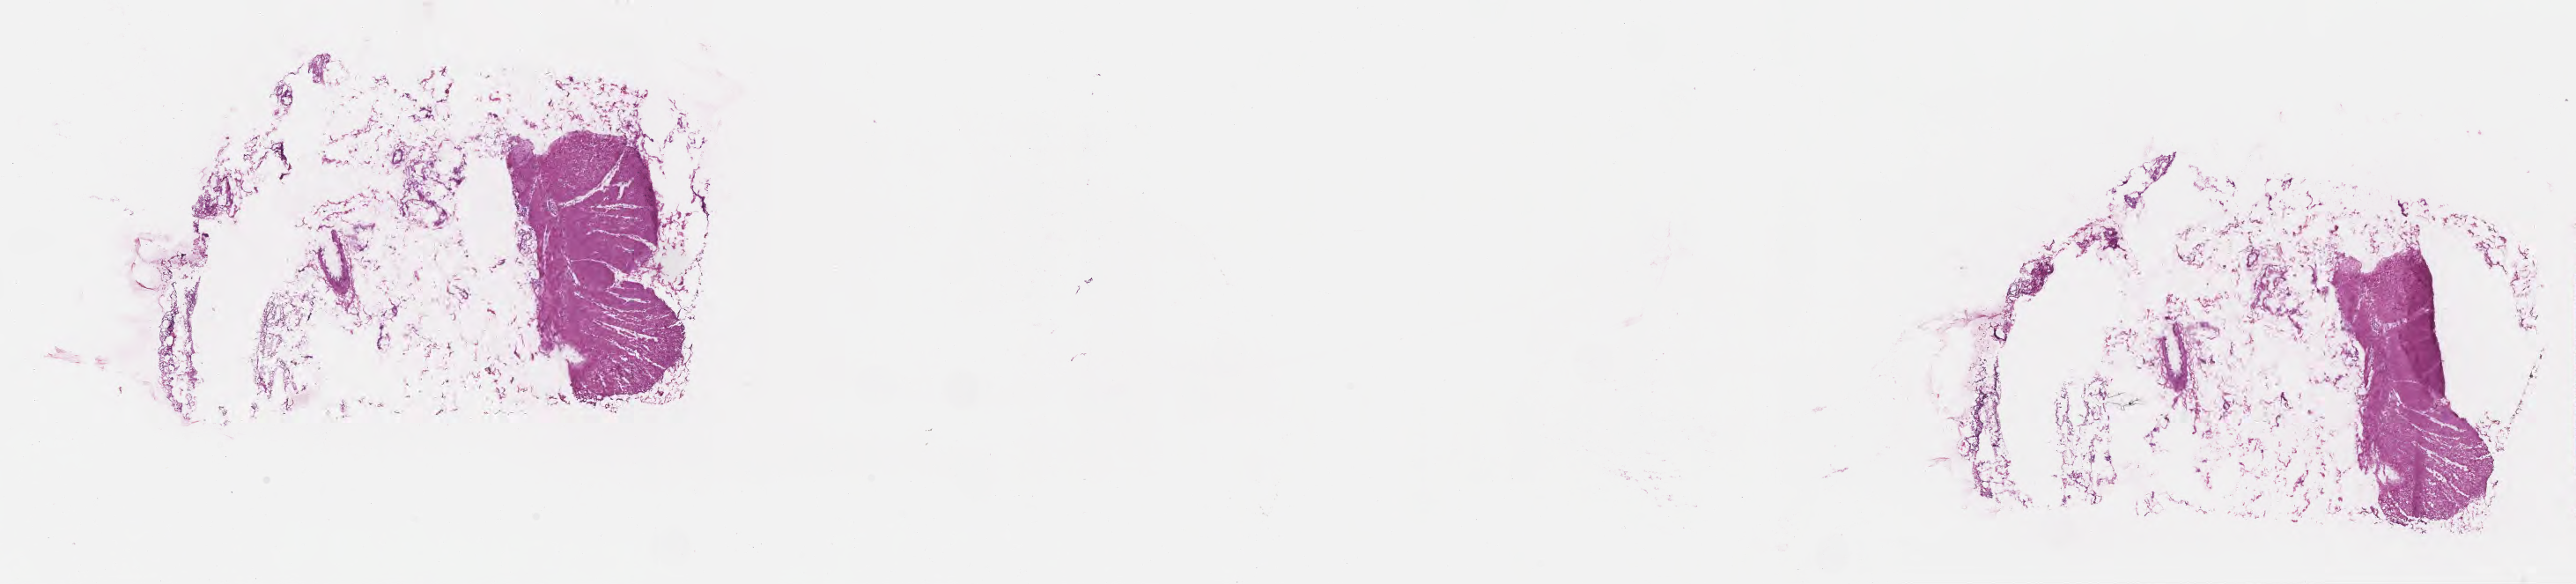
Digitized H&E-stained section — whole scanned area (about 23.6 x 5.4 mm) shown as a low-resolution overview; frozen section (tissue freezing medium); specimen: normal-tissue sample (non-tumor) from a patient with adenocarcinoma, NOS; anatomic site: sigmoid colon. Male, age 82 years at initial diagnosis. Pathologist review of this section (percent, as recorded): tumor cells 0%, tumor nuclei 0%, stromal cells 0%, necrosis 0%, normal cells 100%. Inflammatory infiltration, as recorded: lymphocyte infiltration 0%, monocyte infiltration 0%, neutrophil infiltration 0%.
This section: non-tumor tissue sample; the patient's diagnosis is given above. Section: top of the tissue portion.